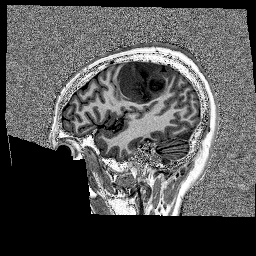
Brain MRI from a brain-tumour surgery series, one sagittal slice; slice 45 of 176 in the series (ordered by position); 1 mm slice thickness; 256 × 256 image matrix, field of view 256 × 256 mm. From the clinical record (not read from this slice): histopathology: Glioblastoma; WHO grade: 4.
Annotated regions visible in this slice (expert manual segmentation):
- tumour: bounding box <118,59,175,103> (left, top, right, bottom; pixels)